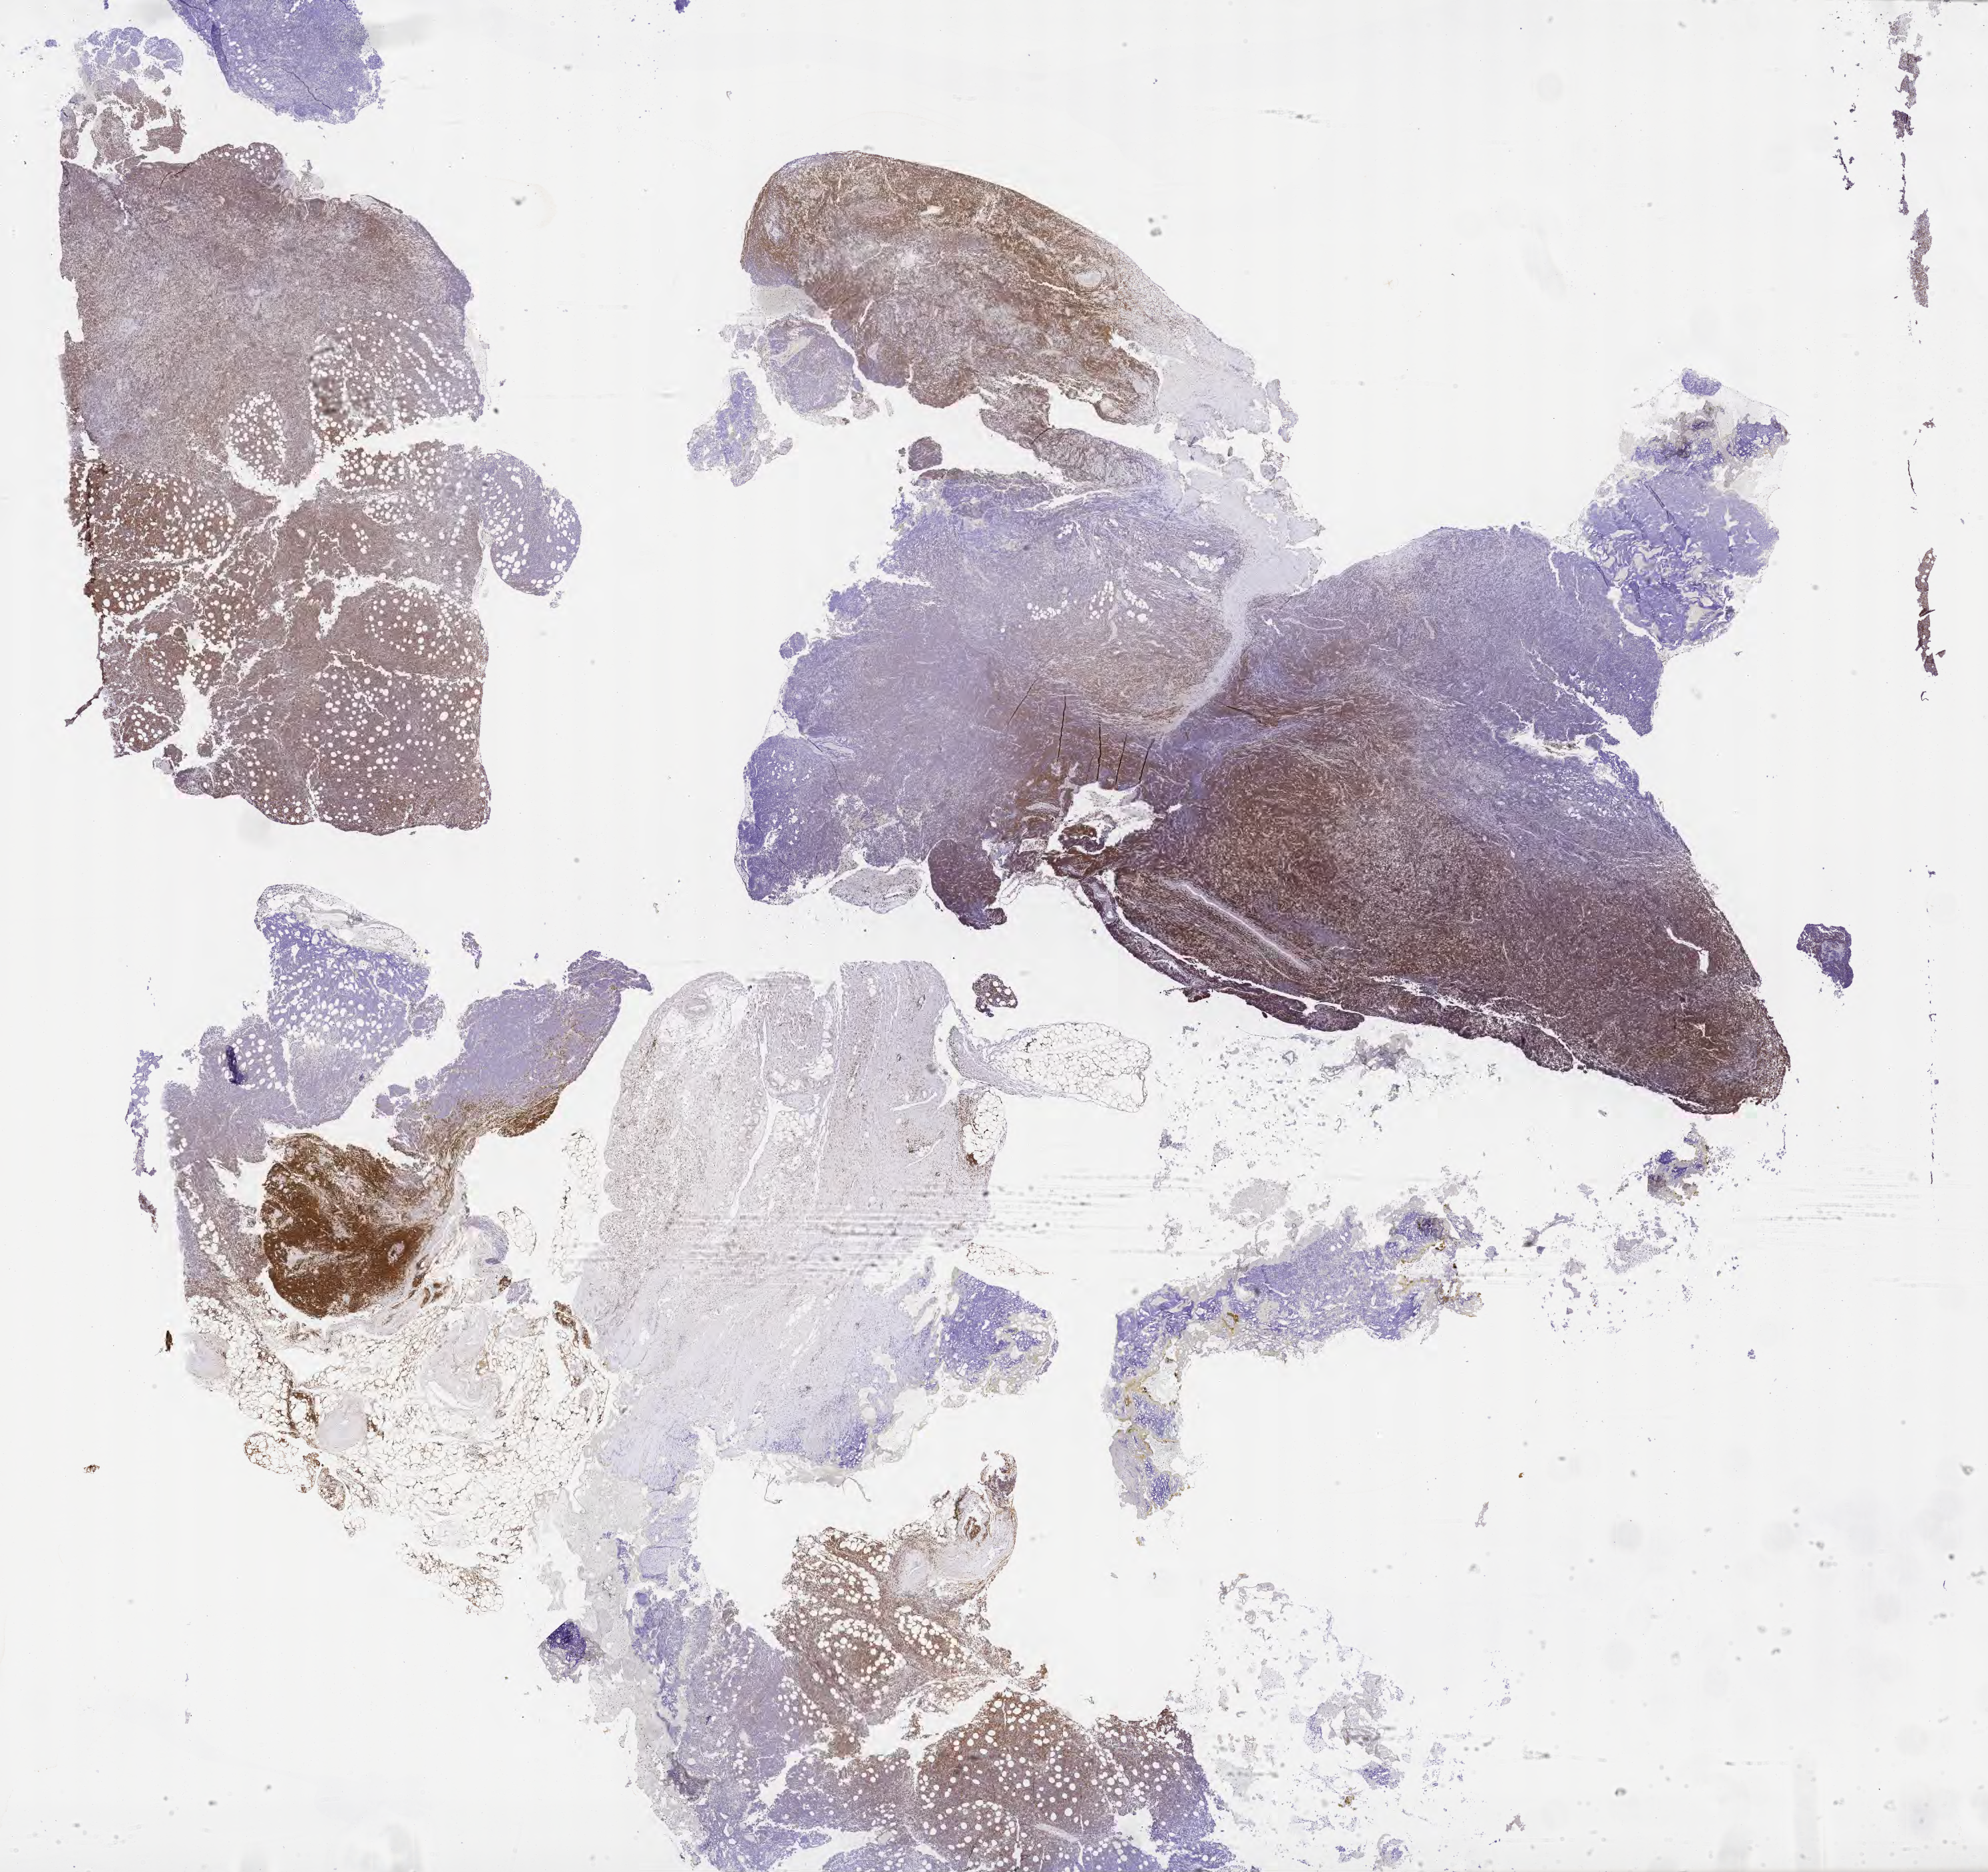
IHC for BCL2, whole-slide image — shown as a low-resolution overview of the whole scanned area (about 24.2 x 22.7 mm). Tumor tissue. Female patient, age 72 years.
Diagnosis: Burkitt lymphoma, NOS.